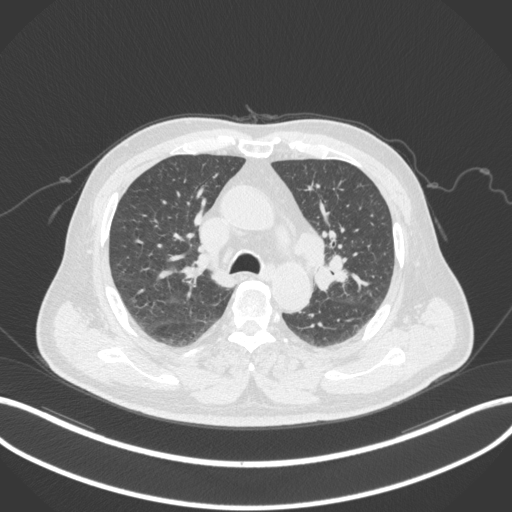
Chest CT, one axial slice; slice 197 of 286 in the series (ordered by position); 120 kVp; lung window (W 1500 / L -600 HU); 1 mm slice thickness; 512 × 512 image matrix, field of view 400 × 400 mm. Male patient, age 67 years. Case-level facts recorded for this patient, not image findings: clinical TNM (as recorded): T2a N1 M0.
Structures marked on this image (bounding box drawn by a radiologist):
- lung tumour (recorded histology: adenocarcinoma): bounding box [x1, y1, x2, y2] px = [311, 252, 353, 291]